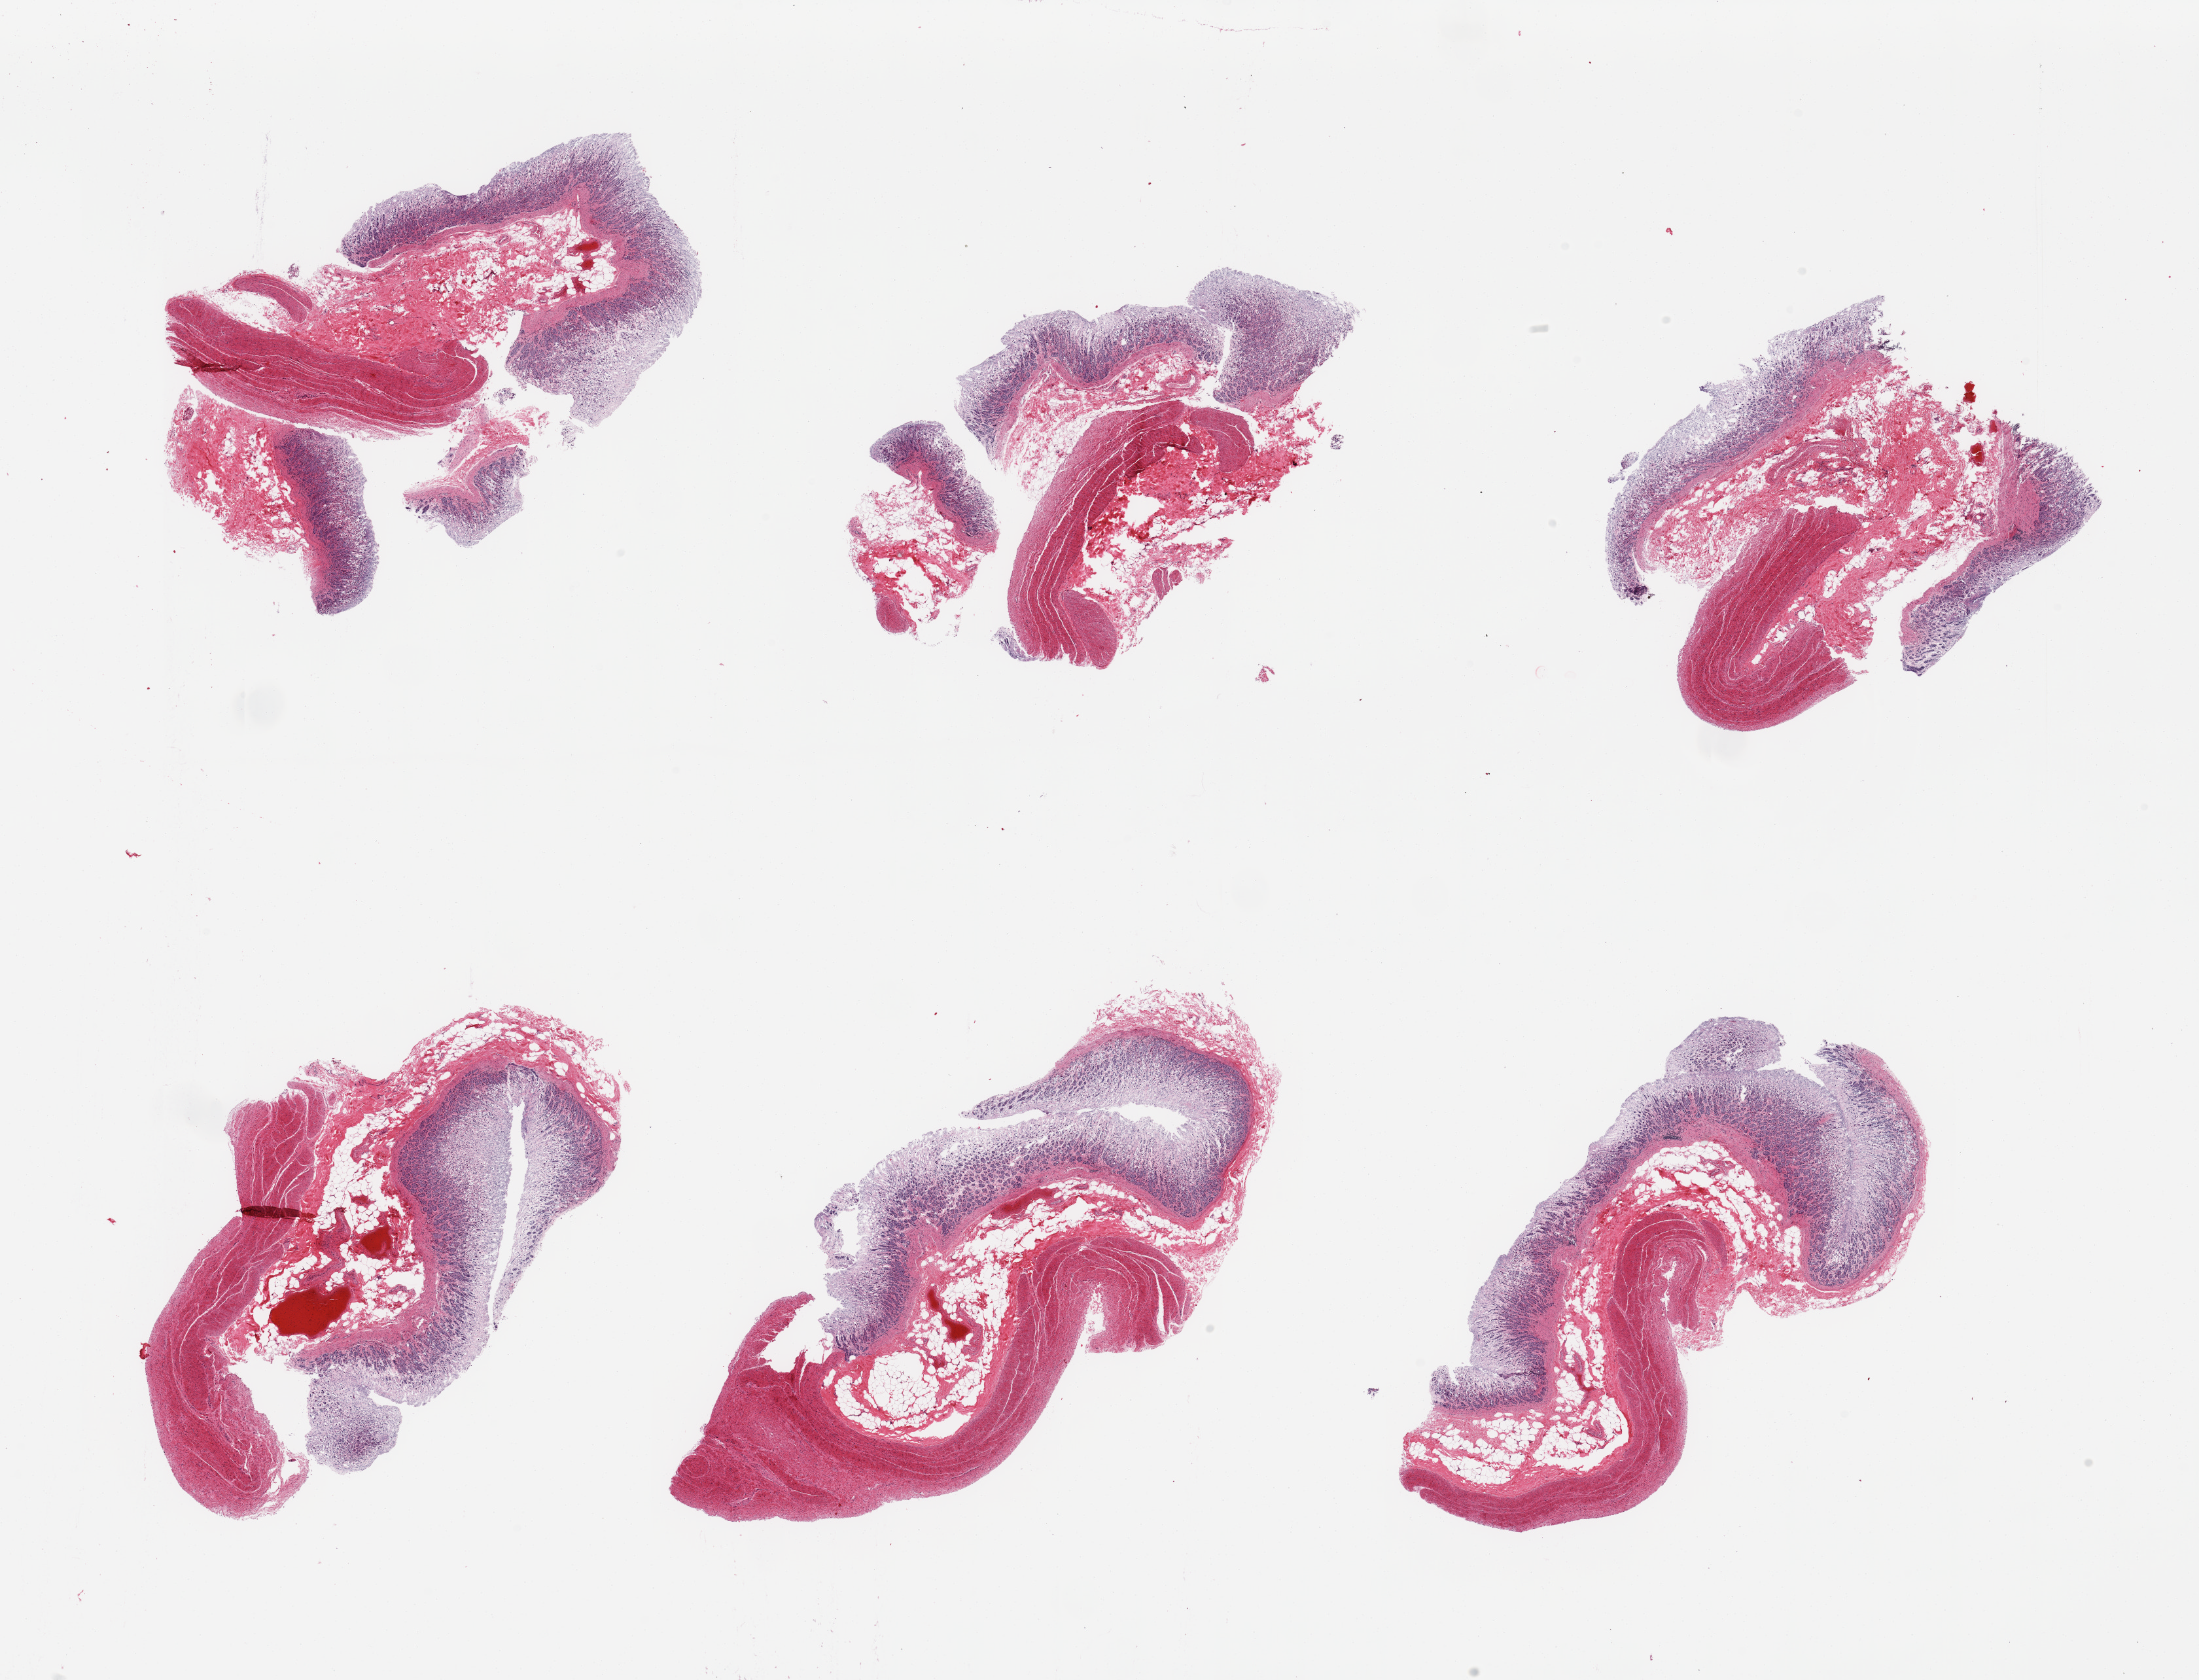
H&E whole-slide image — shown as a low-resolution overview of the whole scanned area (about 26.6 x 20.3 mm); PAXgene-fixed, paraffin-embedded tissue; section of stomach (target tissue); donor tissue sample. Donor sex: male.
- pathologist's review note for this sample: 6 pieces; variably preserved mucosa (2-3), submucosa, and muscularis (1)